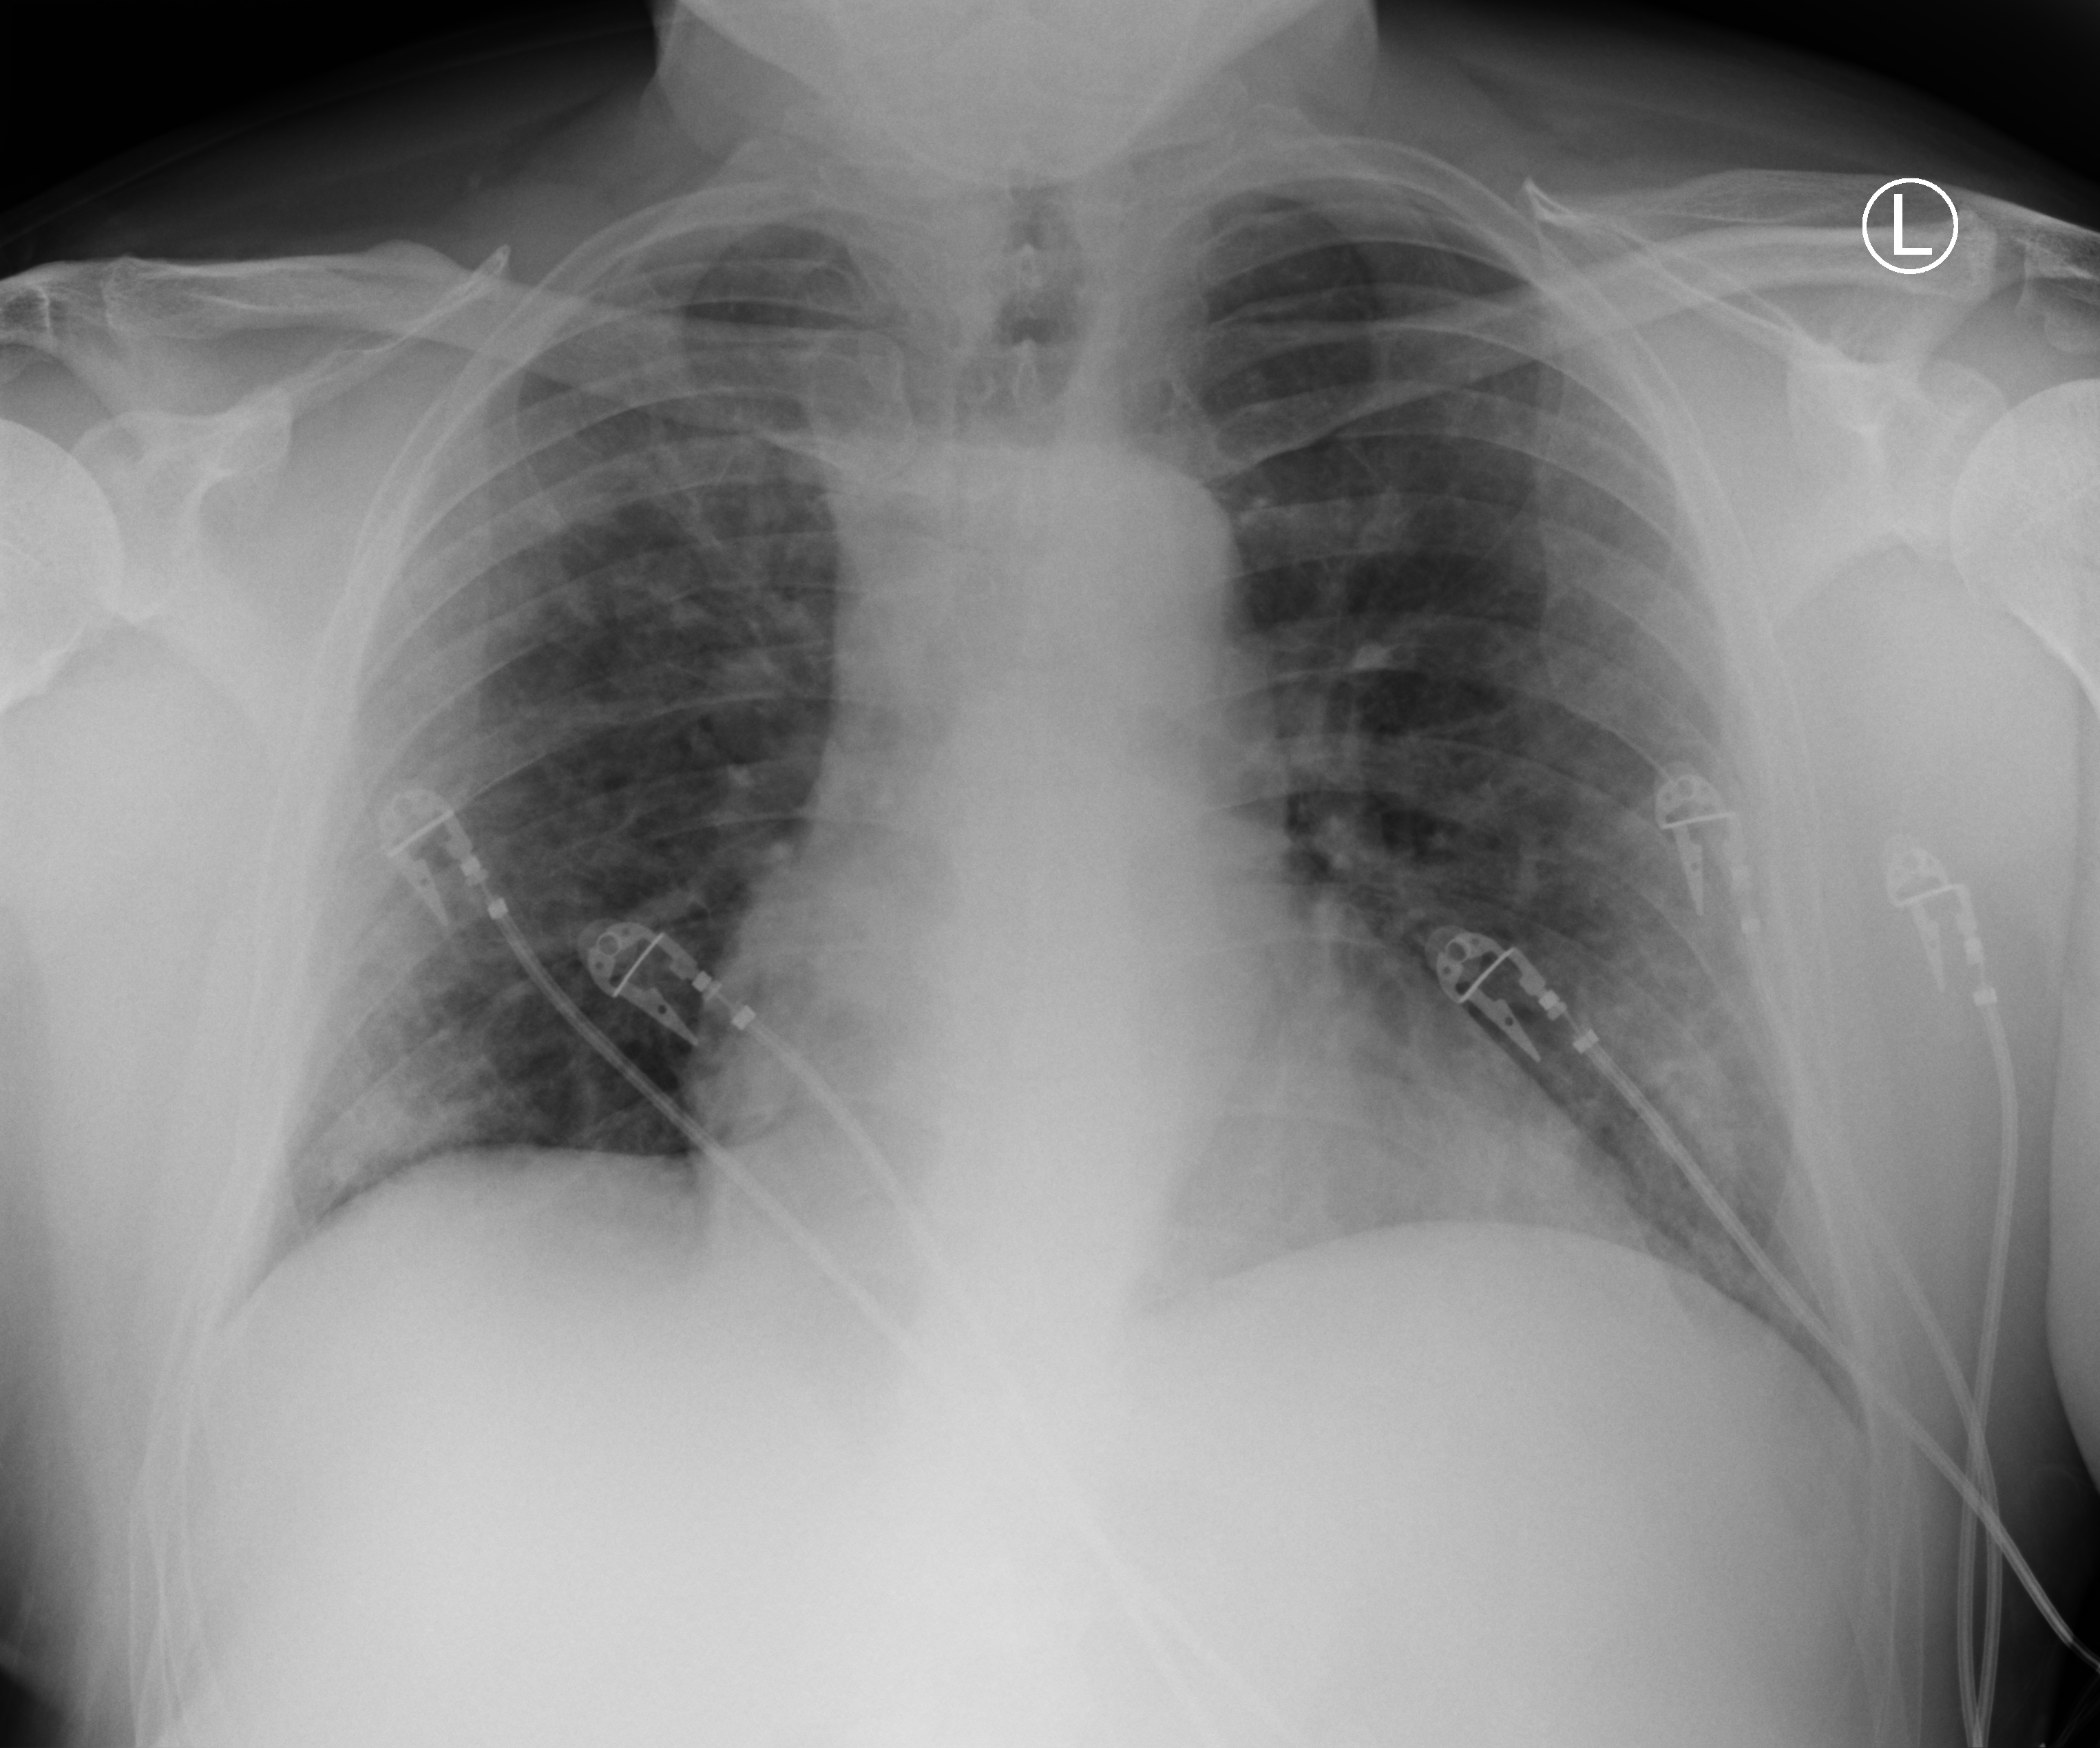
Bedside chest radiograph (computed radiography). Male patient hospitalised with COVID-19, age 18–59 years.
Hospital-stay facts (about this admission, not read from this image; timing relative to this image not recorded): COPD (admission record): no; admitted to intensive care during this hospital stay: no.